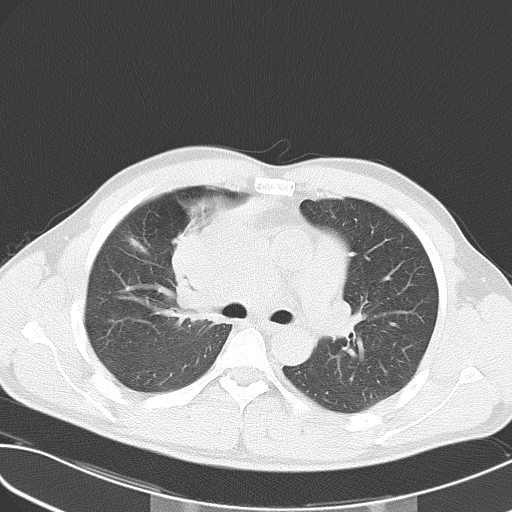
Chest CT, one axial slice. Slice 35 of 55 in the series (ordered by position). Reconstruction kernel B70f. 120 kVp. Lung window (W 1500 / L -600 HU). 5 mm slice thickness. 512 × 512 image matrix, field of view 346 × 346 mm. Male patient, age 32 years. From the clinical record (not read from this slice): clinical TNM (as recorded): T4 N3 M0.
Structures marked on this image (bounding box drawn by a radiologist):
- lung tumour (recorded histology: small cell carcinoma): box from (x=162, y=209) to (x=233, y=331) px